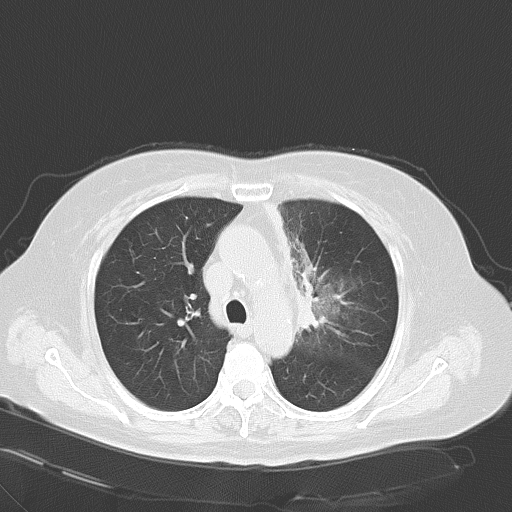
Chest CT, one axial slice. Reconstruction kernel B70f. Lung window (W 1500 / L -600 HU). 512 × 512 image matrix. Patient: female, 65 years. From the clinical record (not read from this slice): clinical TNM (as recorded): T2b N1 M0.
Annotated regions visible in this slice (bounding box drawn by a radiologist):
- lung tumour (recorded histology: adenocarcinoma): bounding box (x1, y1, x2, y2) in pixels: (297, 269, 322, 340)